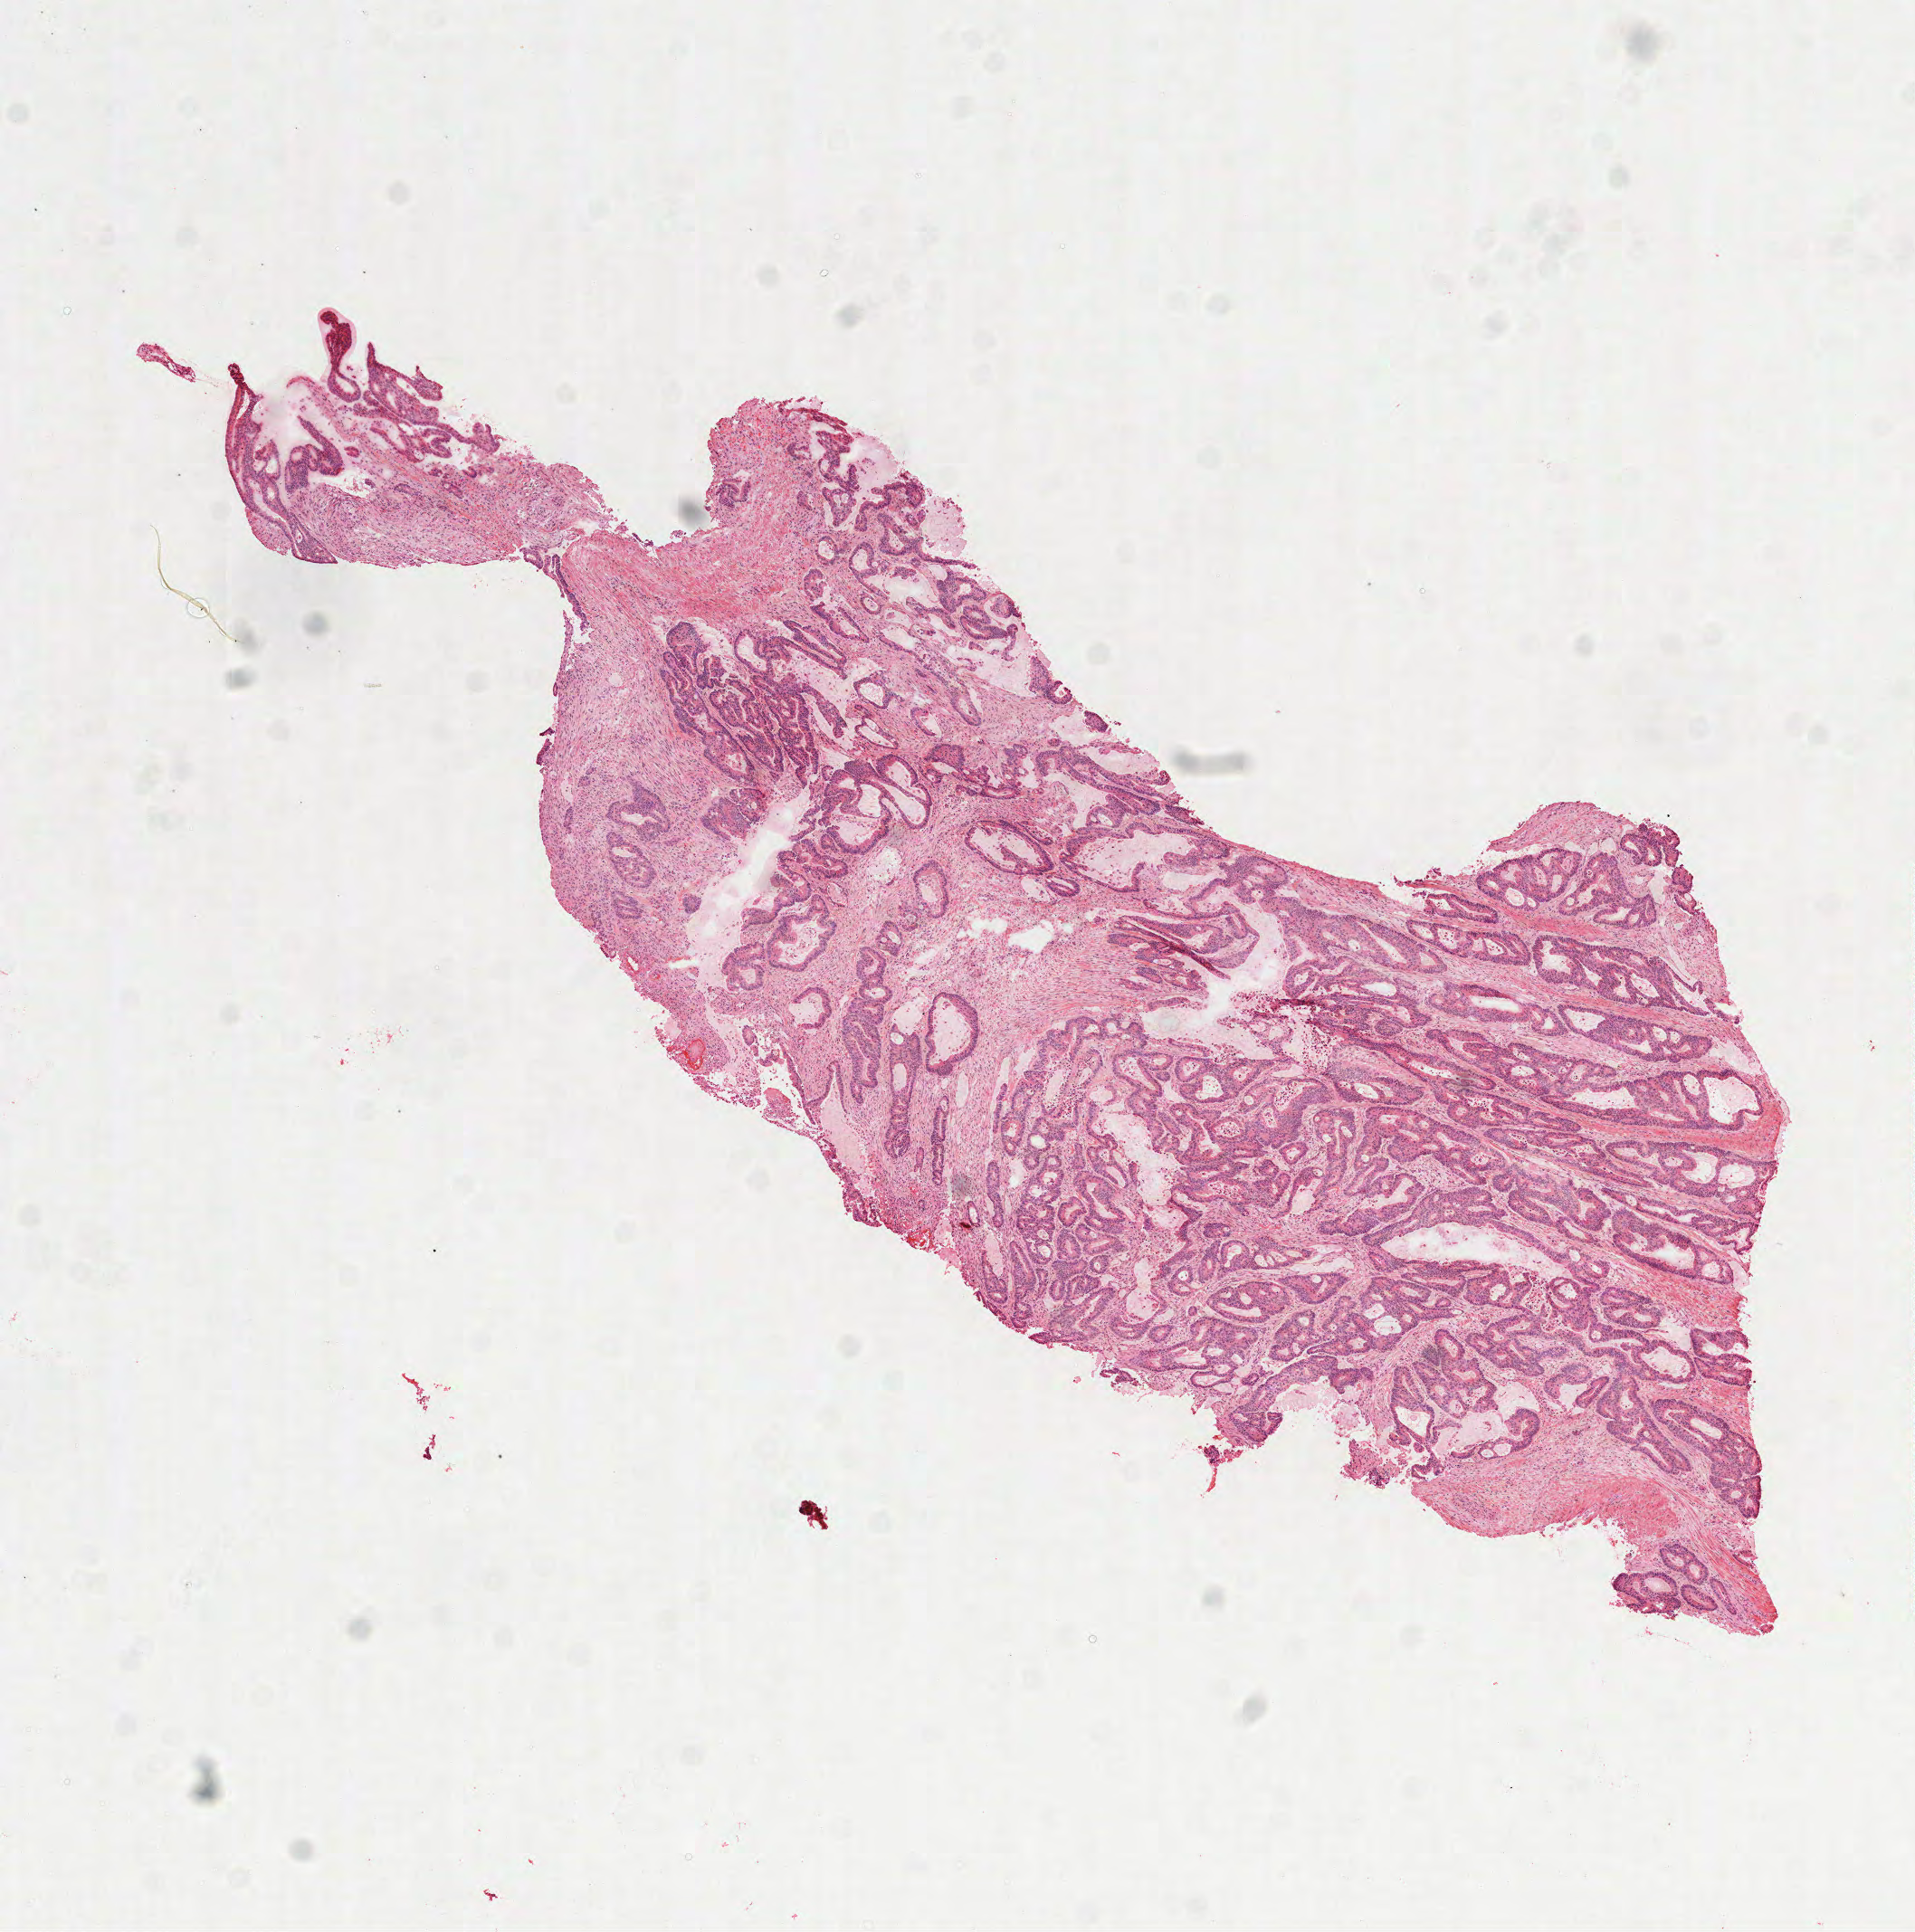
Hematoxylin and eosin (H&E) stained whole-slide image, whole scanned area (about 8.5 x 8.6 mm) shown as a low-resolution overview; frozen section; colon, primary tumour sample. Patient: female, age at initial diagnosis 45 years. Slide review estimates, as recorded: tumour cells 75%, tumour nuclei 75%, normal cells 0%, stromal cells 25%, necrosis 0%.
TNM: T3 N1 M1. AJCC pathologic stage: IV (6th edition). Histologic diagnosis: Mucinous adenocarcinoma (sigmoid colon).